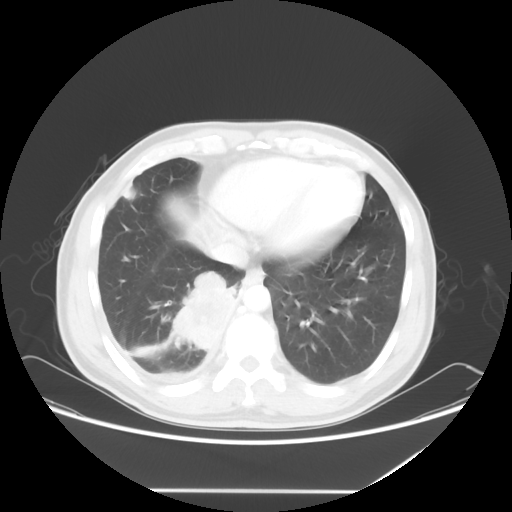
Chest CT, one axial slice; slice 18 of 60 in the series (ordered by position); reconstruction kernel STANDARD; lung window (W 1500 / L -600 HU); 512 × 512 image matrix, field of view 419 × 419 mm. Male patient, age 48 years. From the clinical record (not read from this slice): clinical TNM (as recorded): T3 N3 M1a.
Structures marked on this image (bounding box drawn by a radiologist):
- lung tumour (recorded histology: squamous cell carcinoma): bounding box [x1, y1, x2, y2] px = [167, 267, 233, 355]